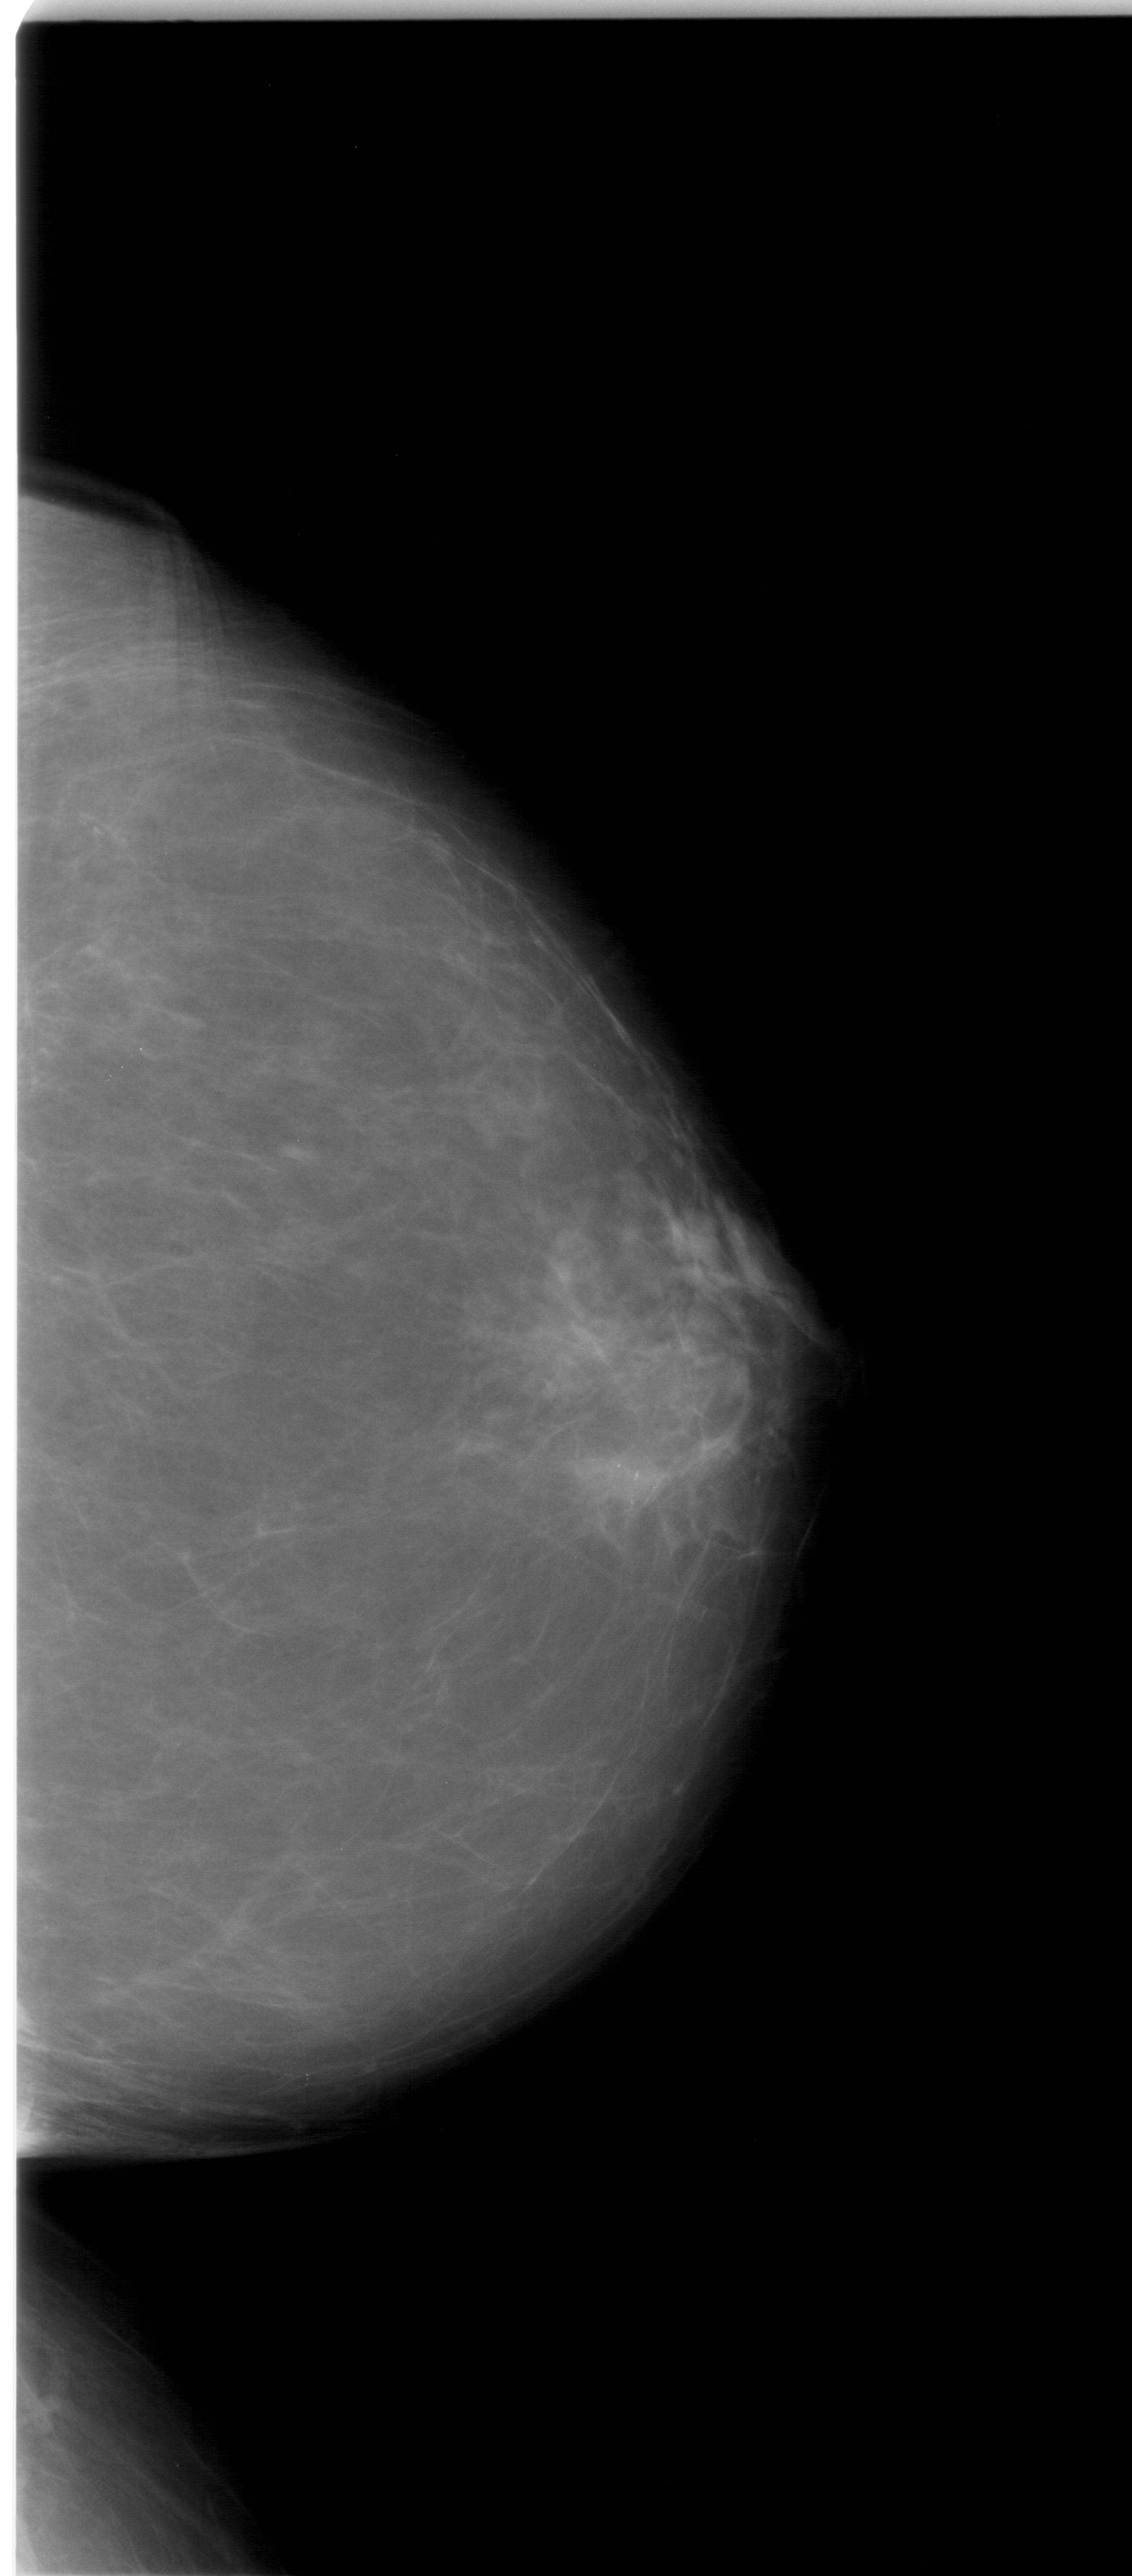
Scanned film-screen mammogram; right breast; craniocaudal (CC) view; breast composition: almost entirely fatty (BI-RADS density category 1 of 4).
Marked findings (only marked abnormalities are described; nothing is implied about the rest of the image): calcifications, morphology pleomorphic, distribution clustered; BI-RADS assessment category 4; subtlety rating 3 on a 1 (subtle) to 5 (obvious) scale; pathology (as recorded): malignant.